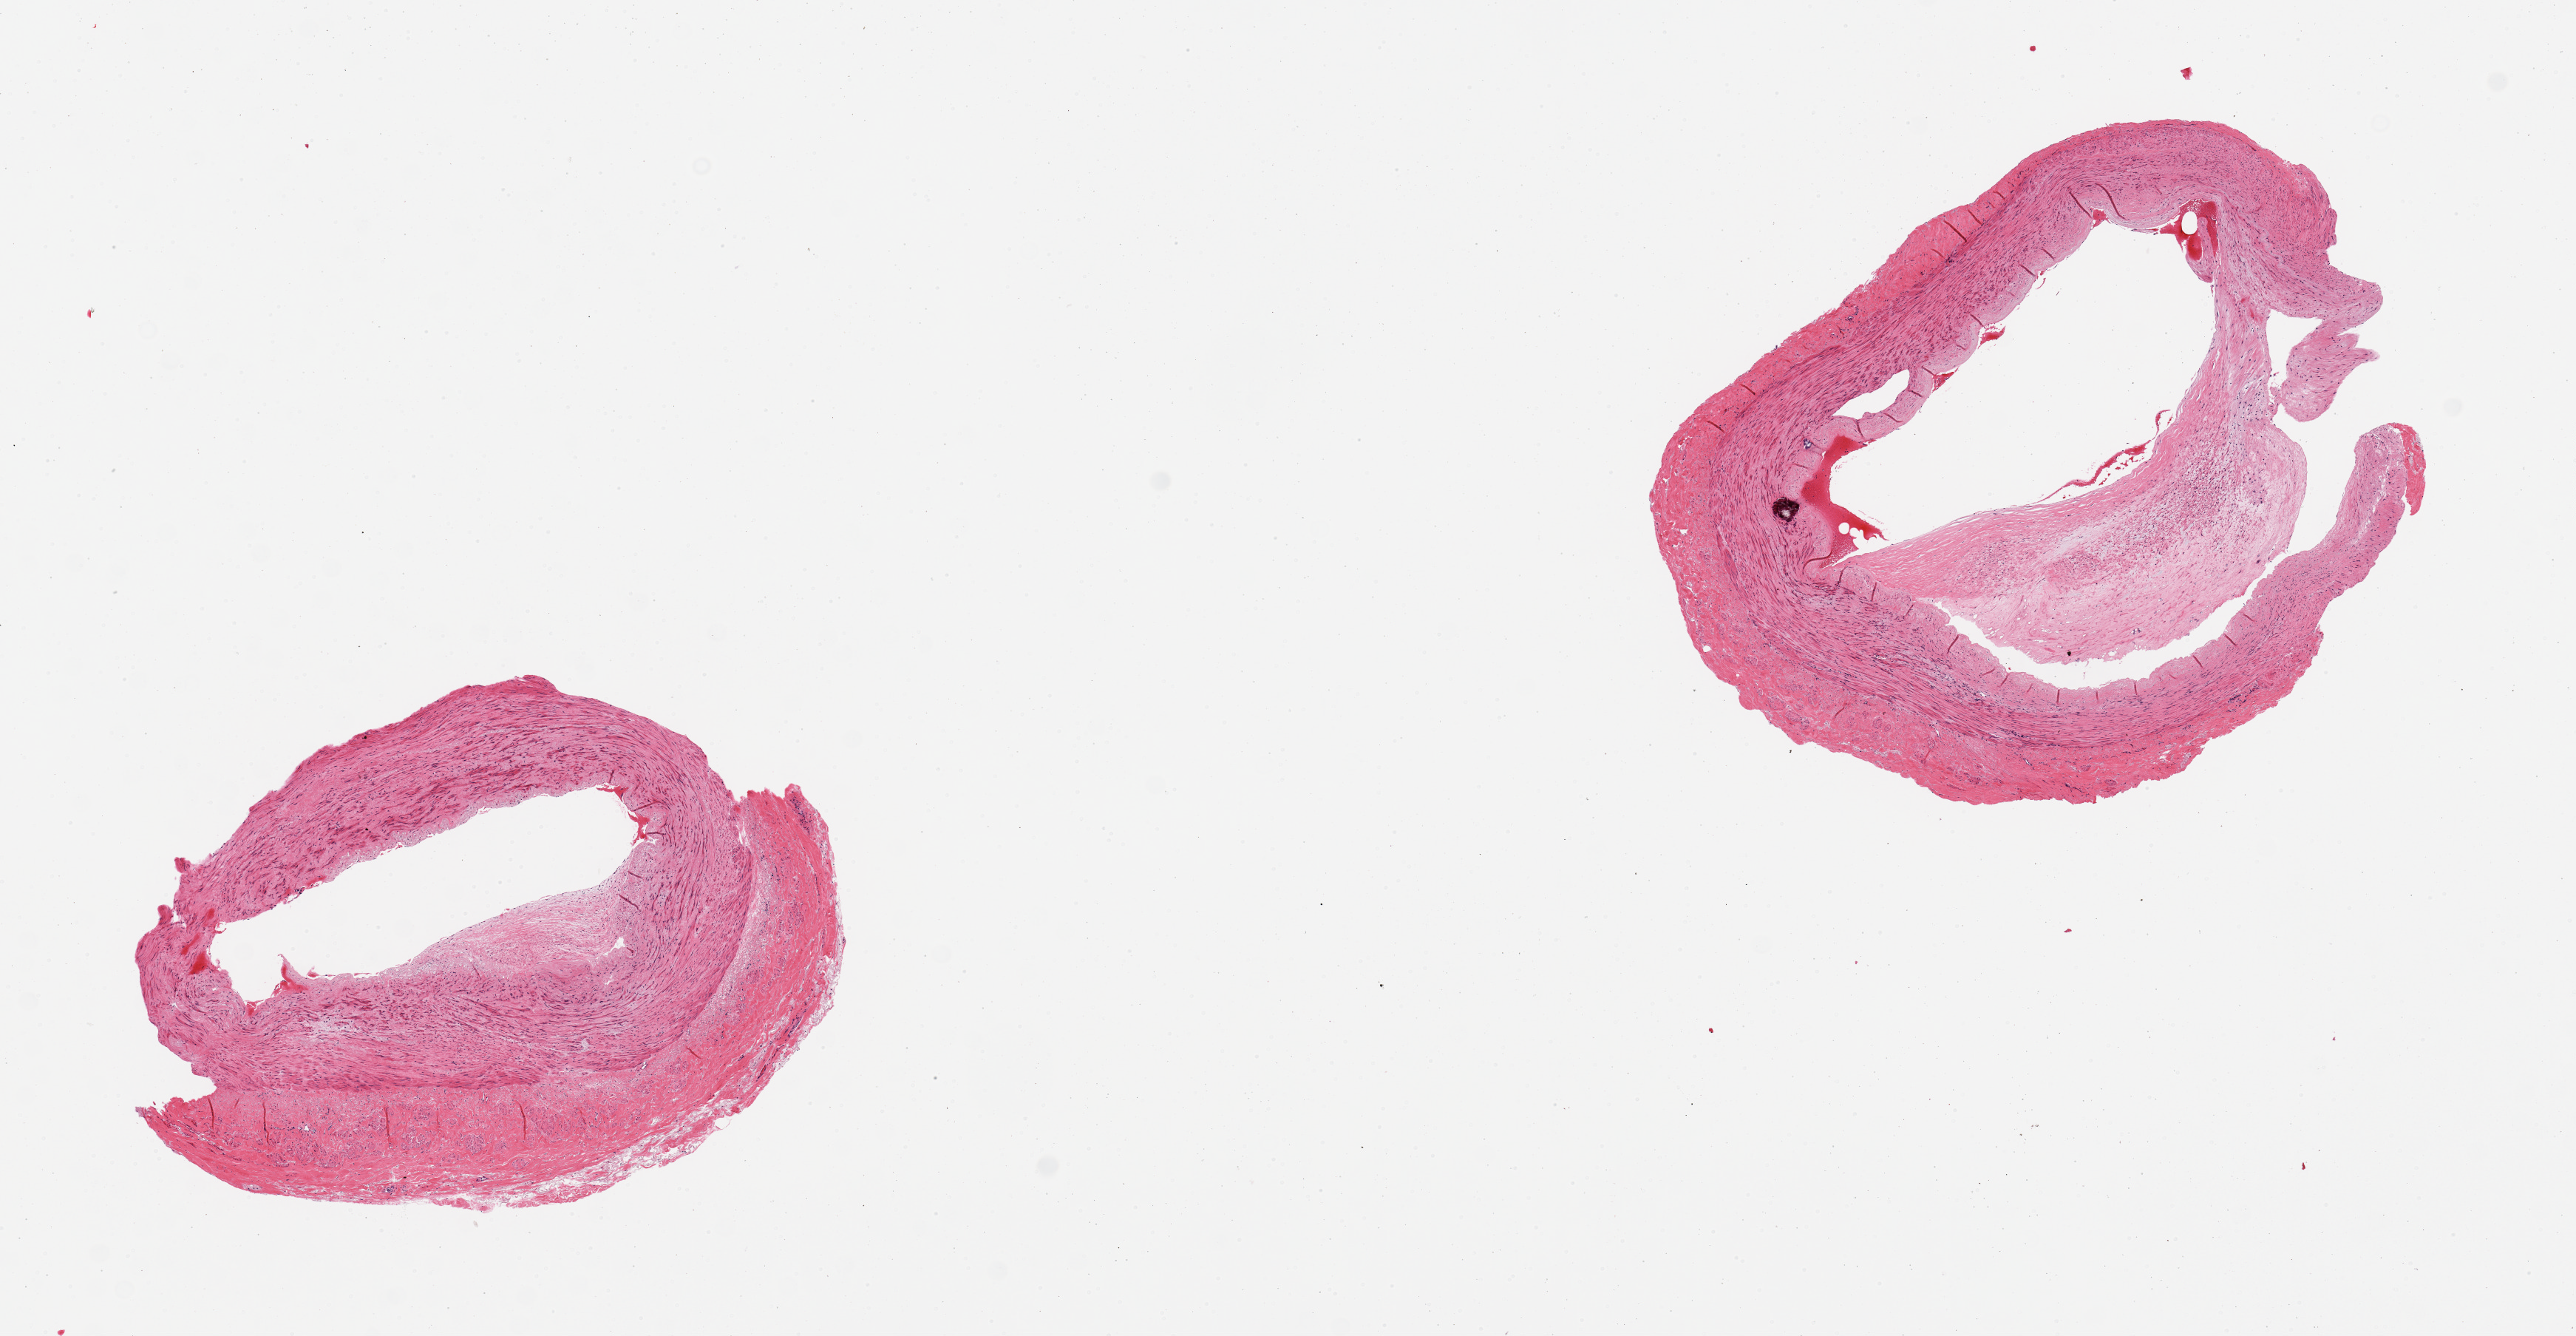
Hematoxylin and eosin (H&E) whole-slide image — low-resolution overview of the scanned area, about 13.8 x 7.1 mm (slide scanned at 20x); PAXgene-fixed, paraffin-embedded tissue; section of tibial artery (target tissue); tissue donor sample. Donor sex: female.
Reviewer comment on this tissue sample: 2 pieces, one section with adherent fibrous tissue up to ~0.5mm.